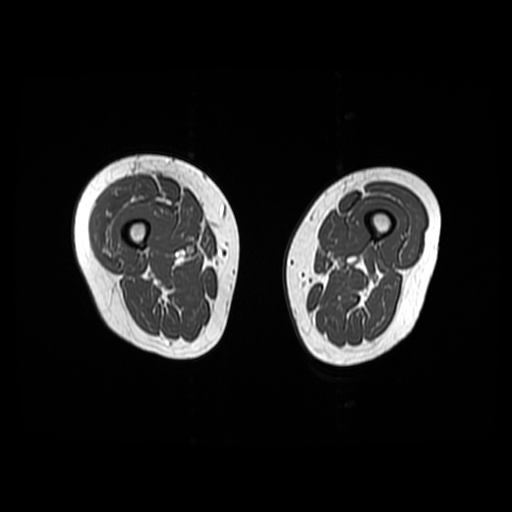
MRI of an extremity soft-tissue mass, one axial slice. Position 15 of 48 along the scan axis. 512 × 512 image matrix, field of view 440 × 440 mm. Female patient. Case-level facts recorded for this patient, not image findings: histological type: pleiomorphic undifferentiated sarcoma; grade: high; site of the primary tumour: right quadricep.
Annotated regions visible in this slice (outlined manually by an expert reader):
- gross tumour volume including surrounding oedema: bounding box <92,174,157,255> (left, top, right, bottom; pixels)